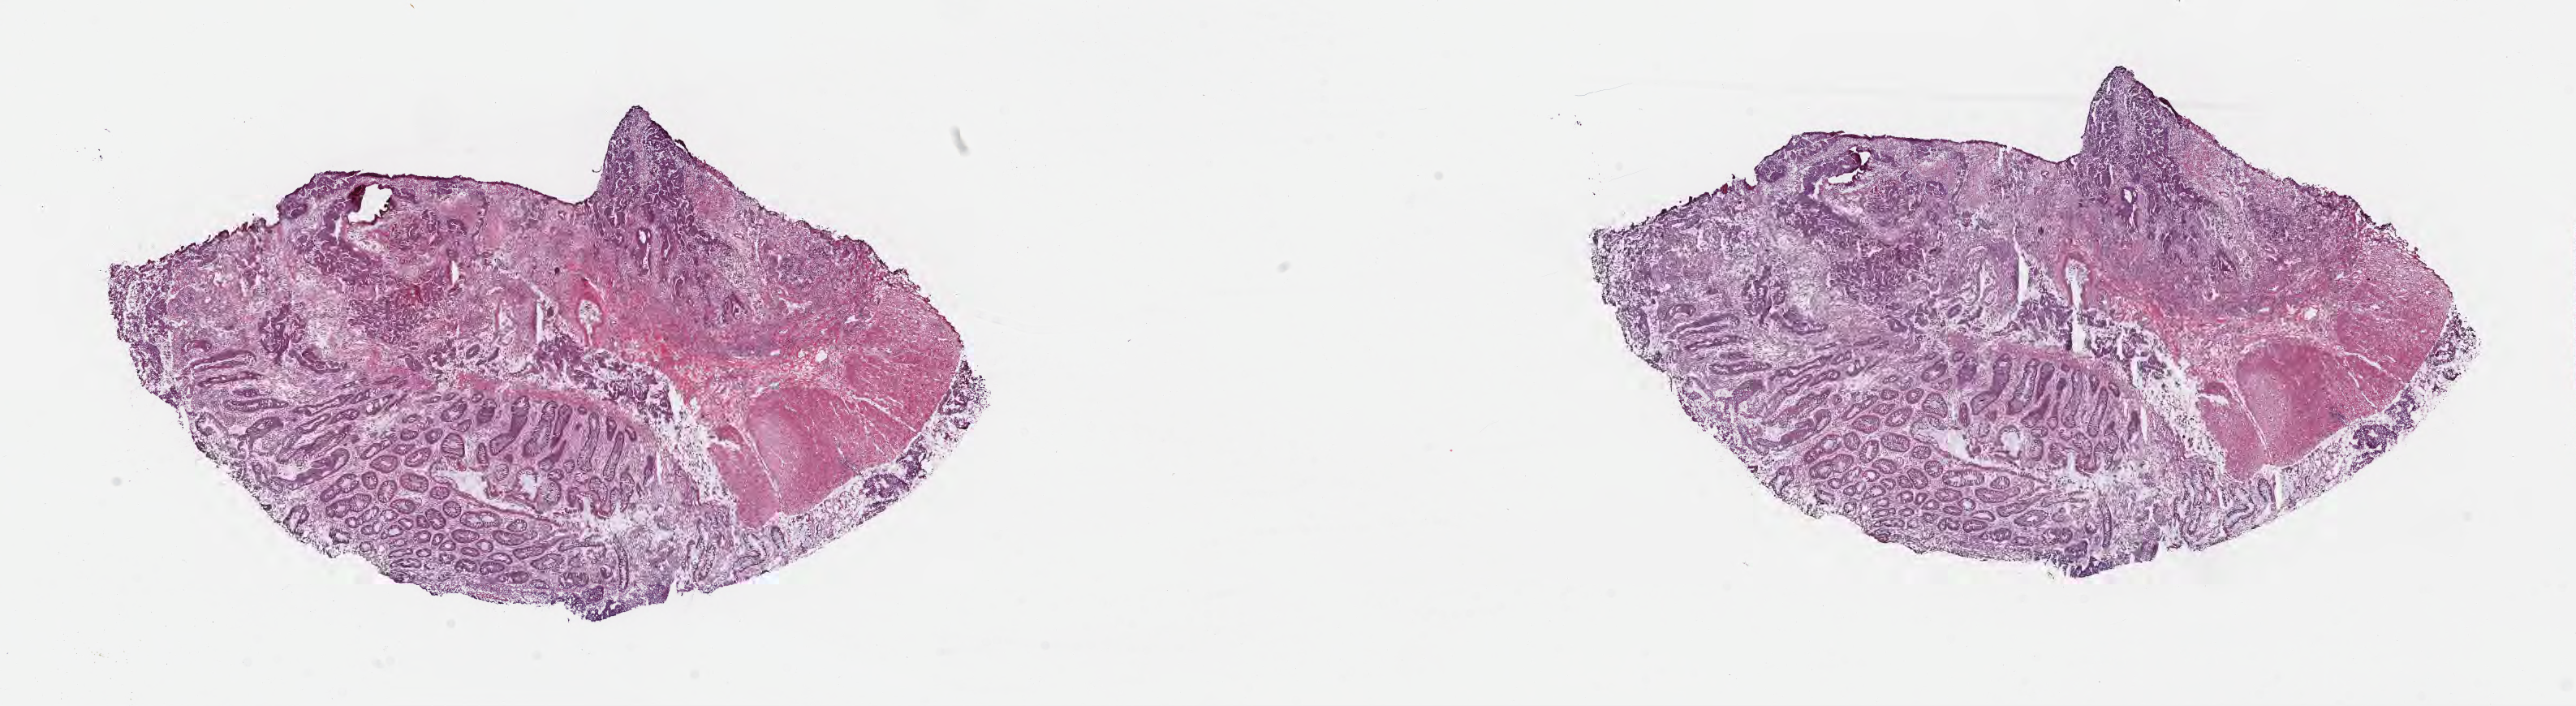
Hematoxylin and eosin (H&E) whole-slide image, shown as a low-resolution overview of the whole scanned area (about 25.7 x 7.0 mm); frozen section (tissue freezing medium); specimen: primary tumor; anatomic site: rectum. Patient: male, age at initial diagnosis 57 years. Tumor grade: G2 (moderately differentiated). Pathologist review of this section (percent, as recorded): tumor cells 65%, tumor nuclei 65%, stromal cells 25%, necrosis 2%, normal cells 8%. Inflammatory infiltration, as recorded: lymphocyte infiltration 6%, monocyte infiltration 4%, neutrophil infiltration 8%.
• section: top of the tissue portion
• diagnosis: Adenocarcinoma, NOS
• AJCC pathologic stage: Stage IIA